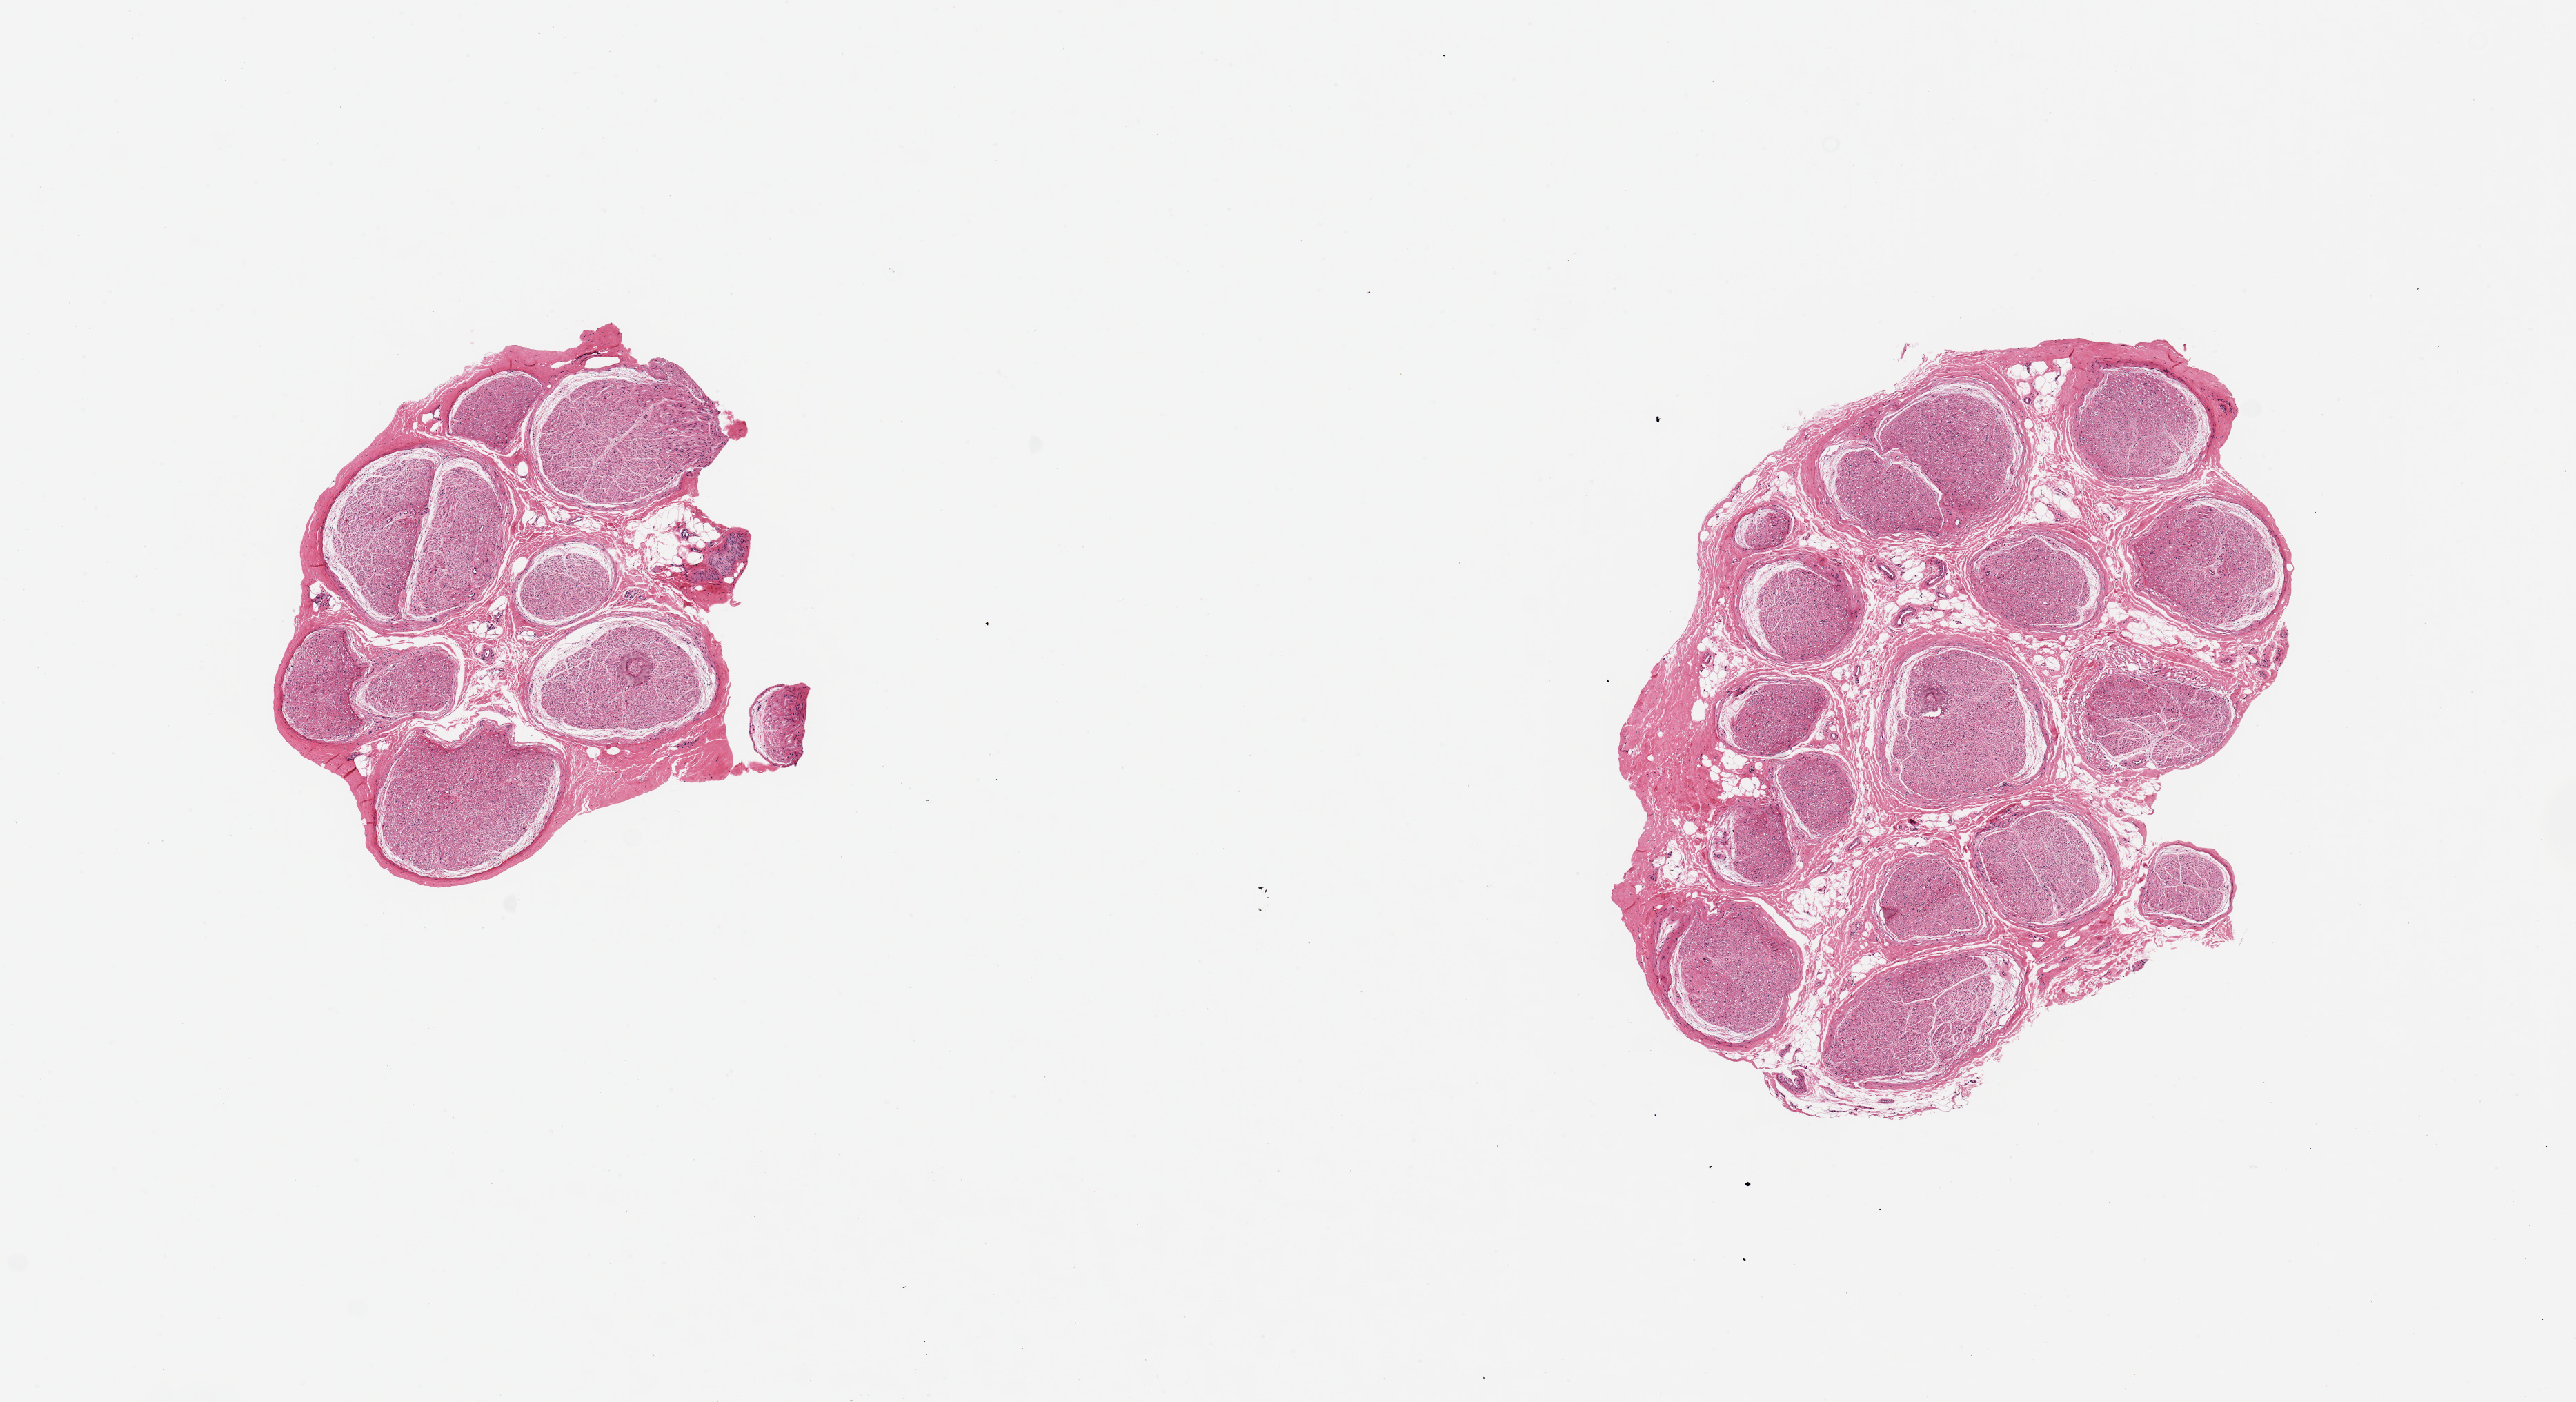
Digitized H&E-stained section, whole scanned area (about 14.8 x 8.0 mm) shown as a low-resolution overview, PAXgene-fixed paraffin-embedded (PFPE) section, sampled site (target tissue): tibial nerve, donor tissue sample. Female donor.
Pathologist's review note for this sample: 2 pieces ~4mm d. Excellent clean specimens.